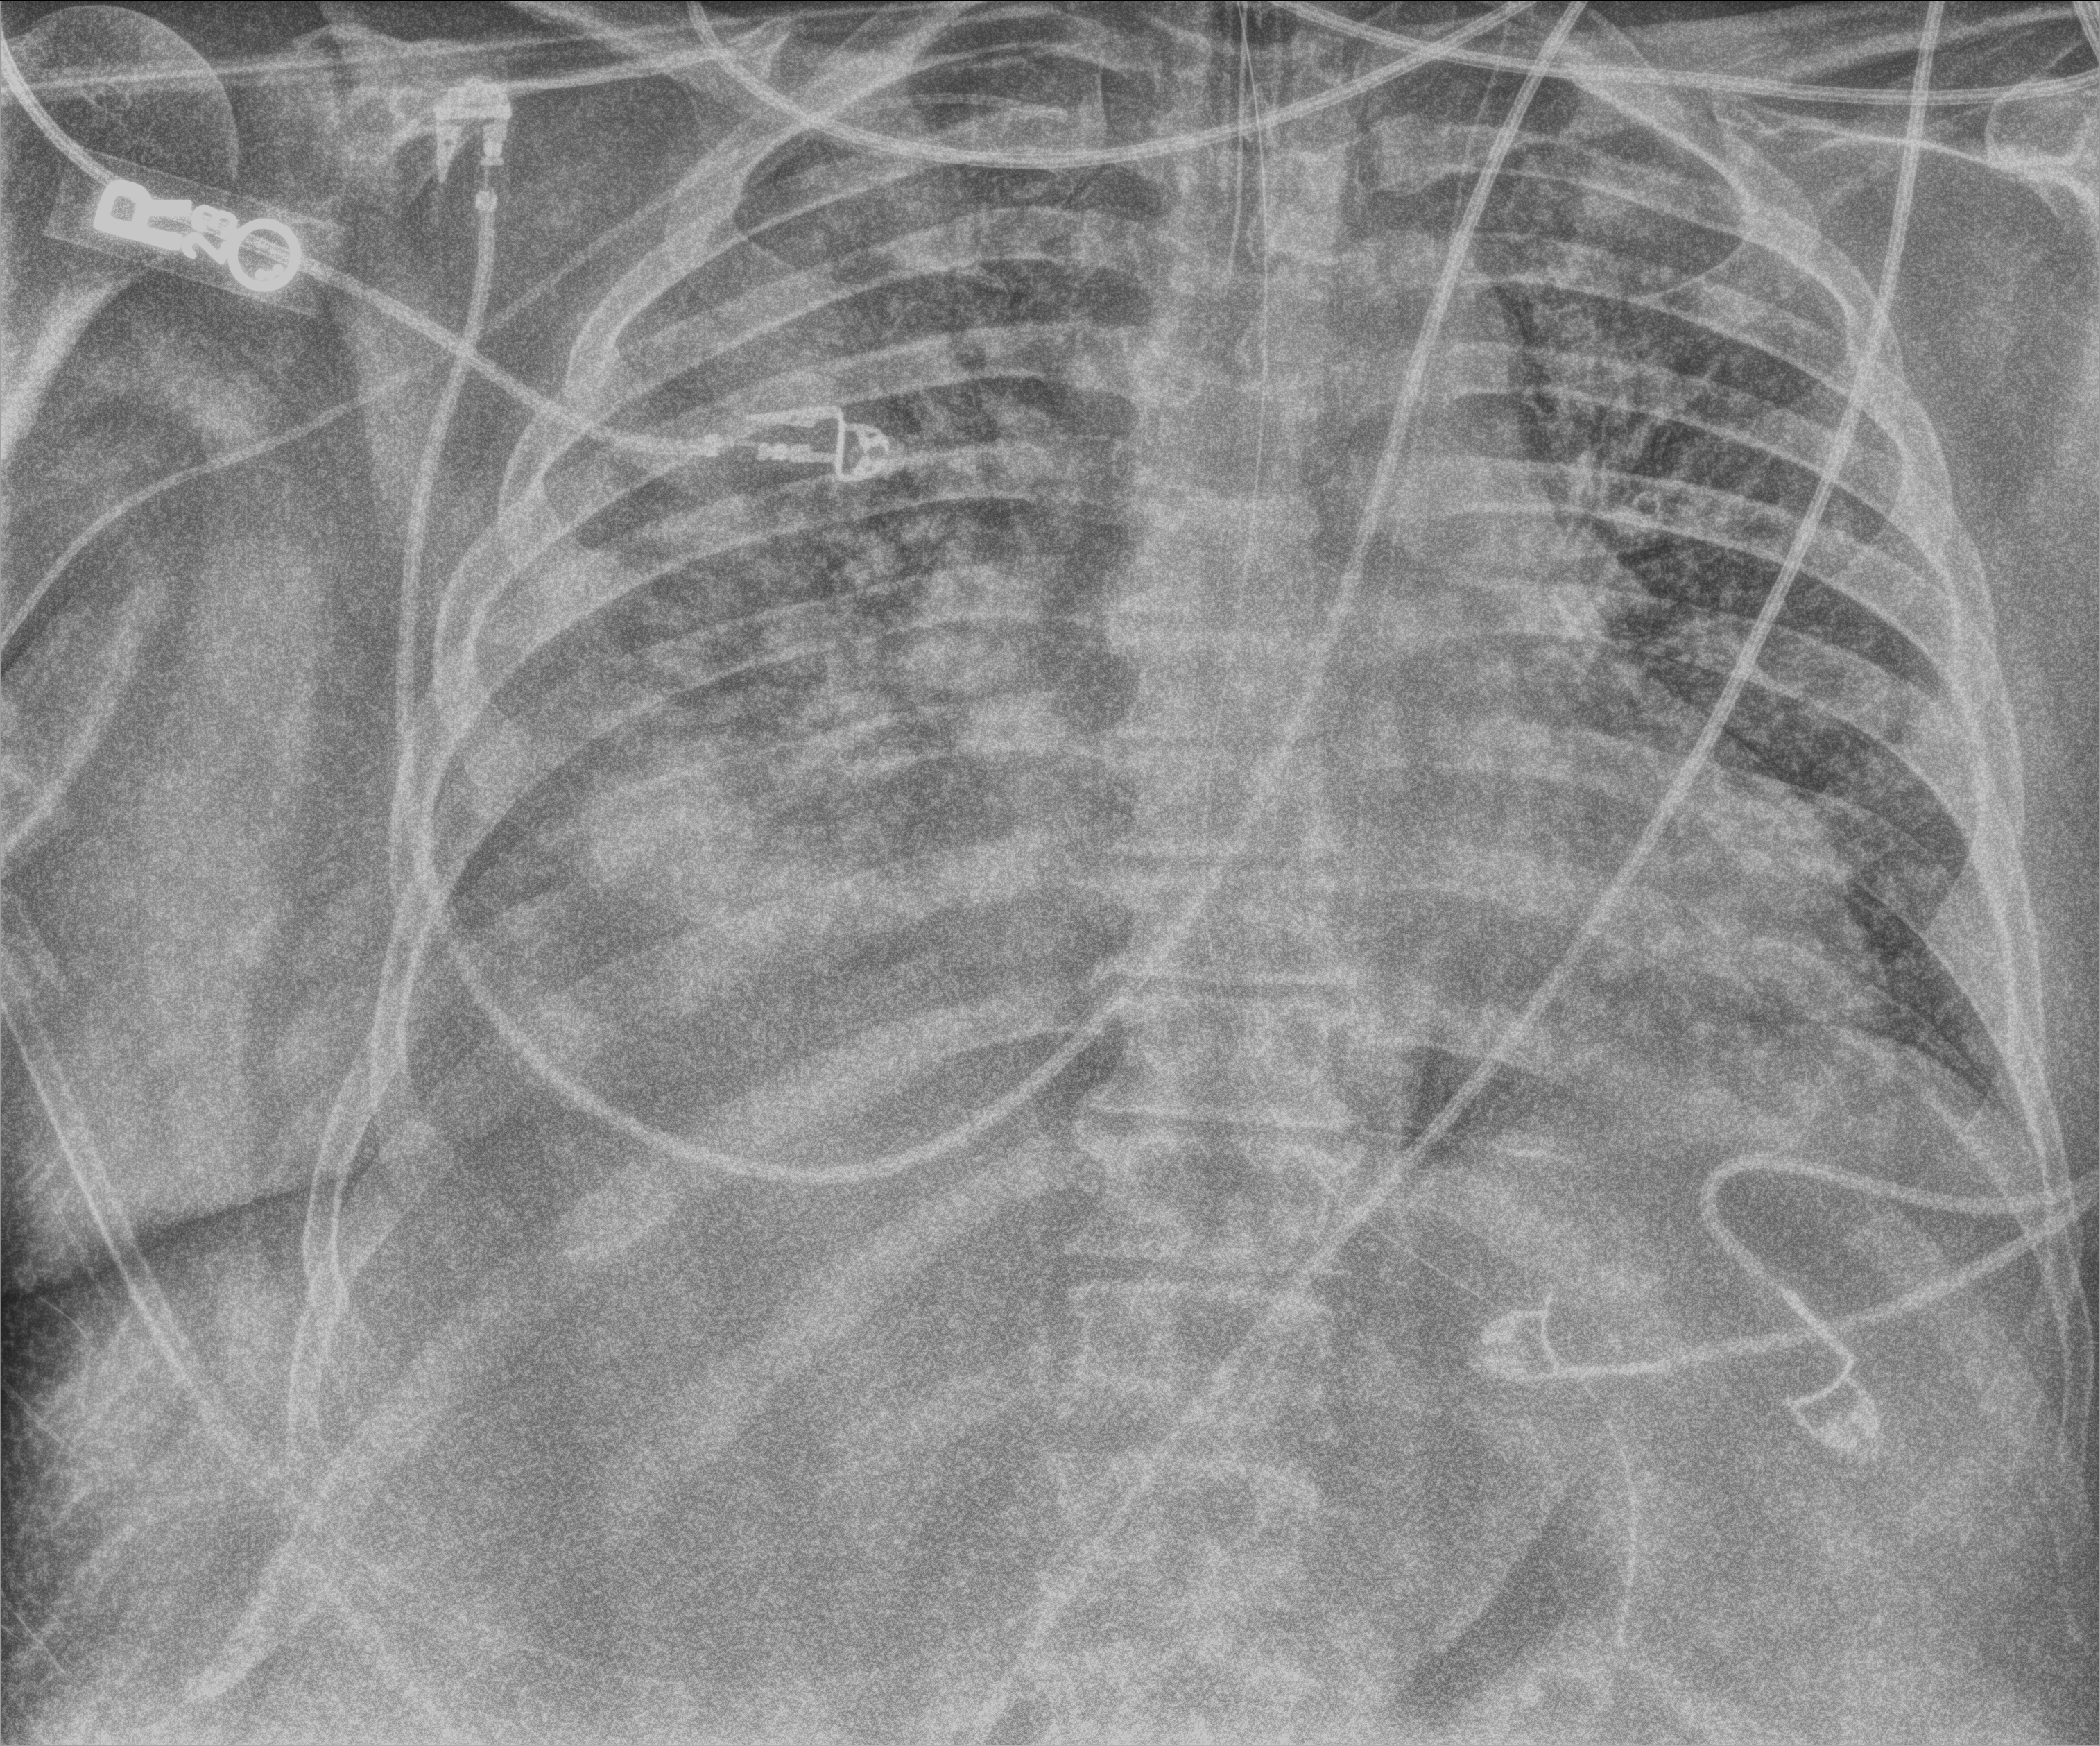
Portable chest radiograph; anteroposterior (AP) projection. Male patient hospitalised with COVID-19, age 18–59 years.
From the hospital-stay record, not from the radiograph (when in the stay this image was taken is not recorded):
- smoking status (admission record): never
- diabetes (admission record): yes
- admitted to intensive care during this hospital stay: yes